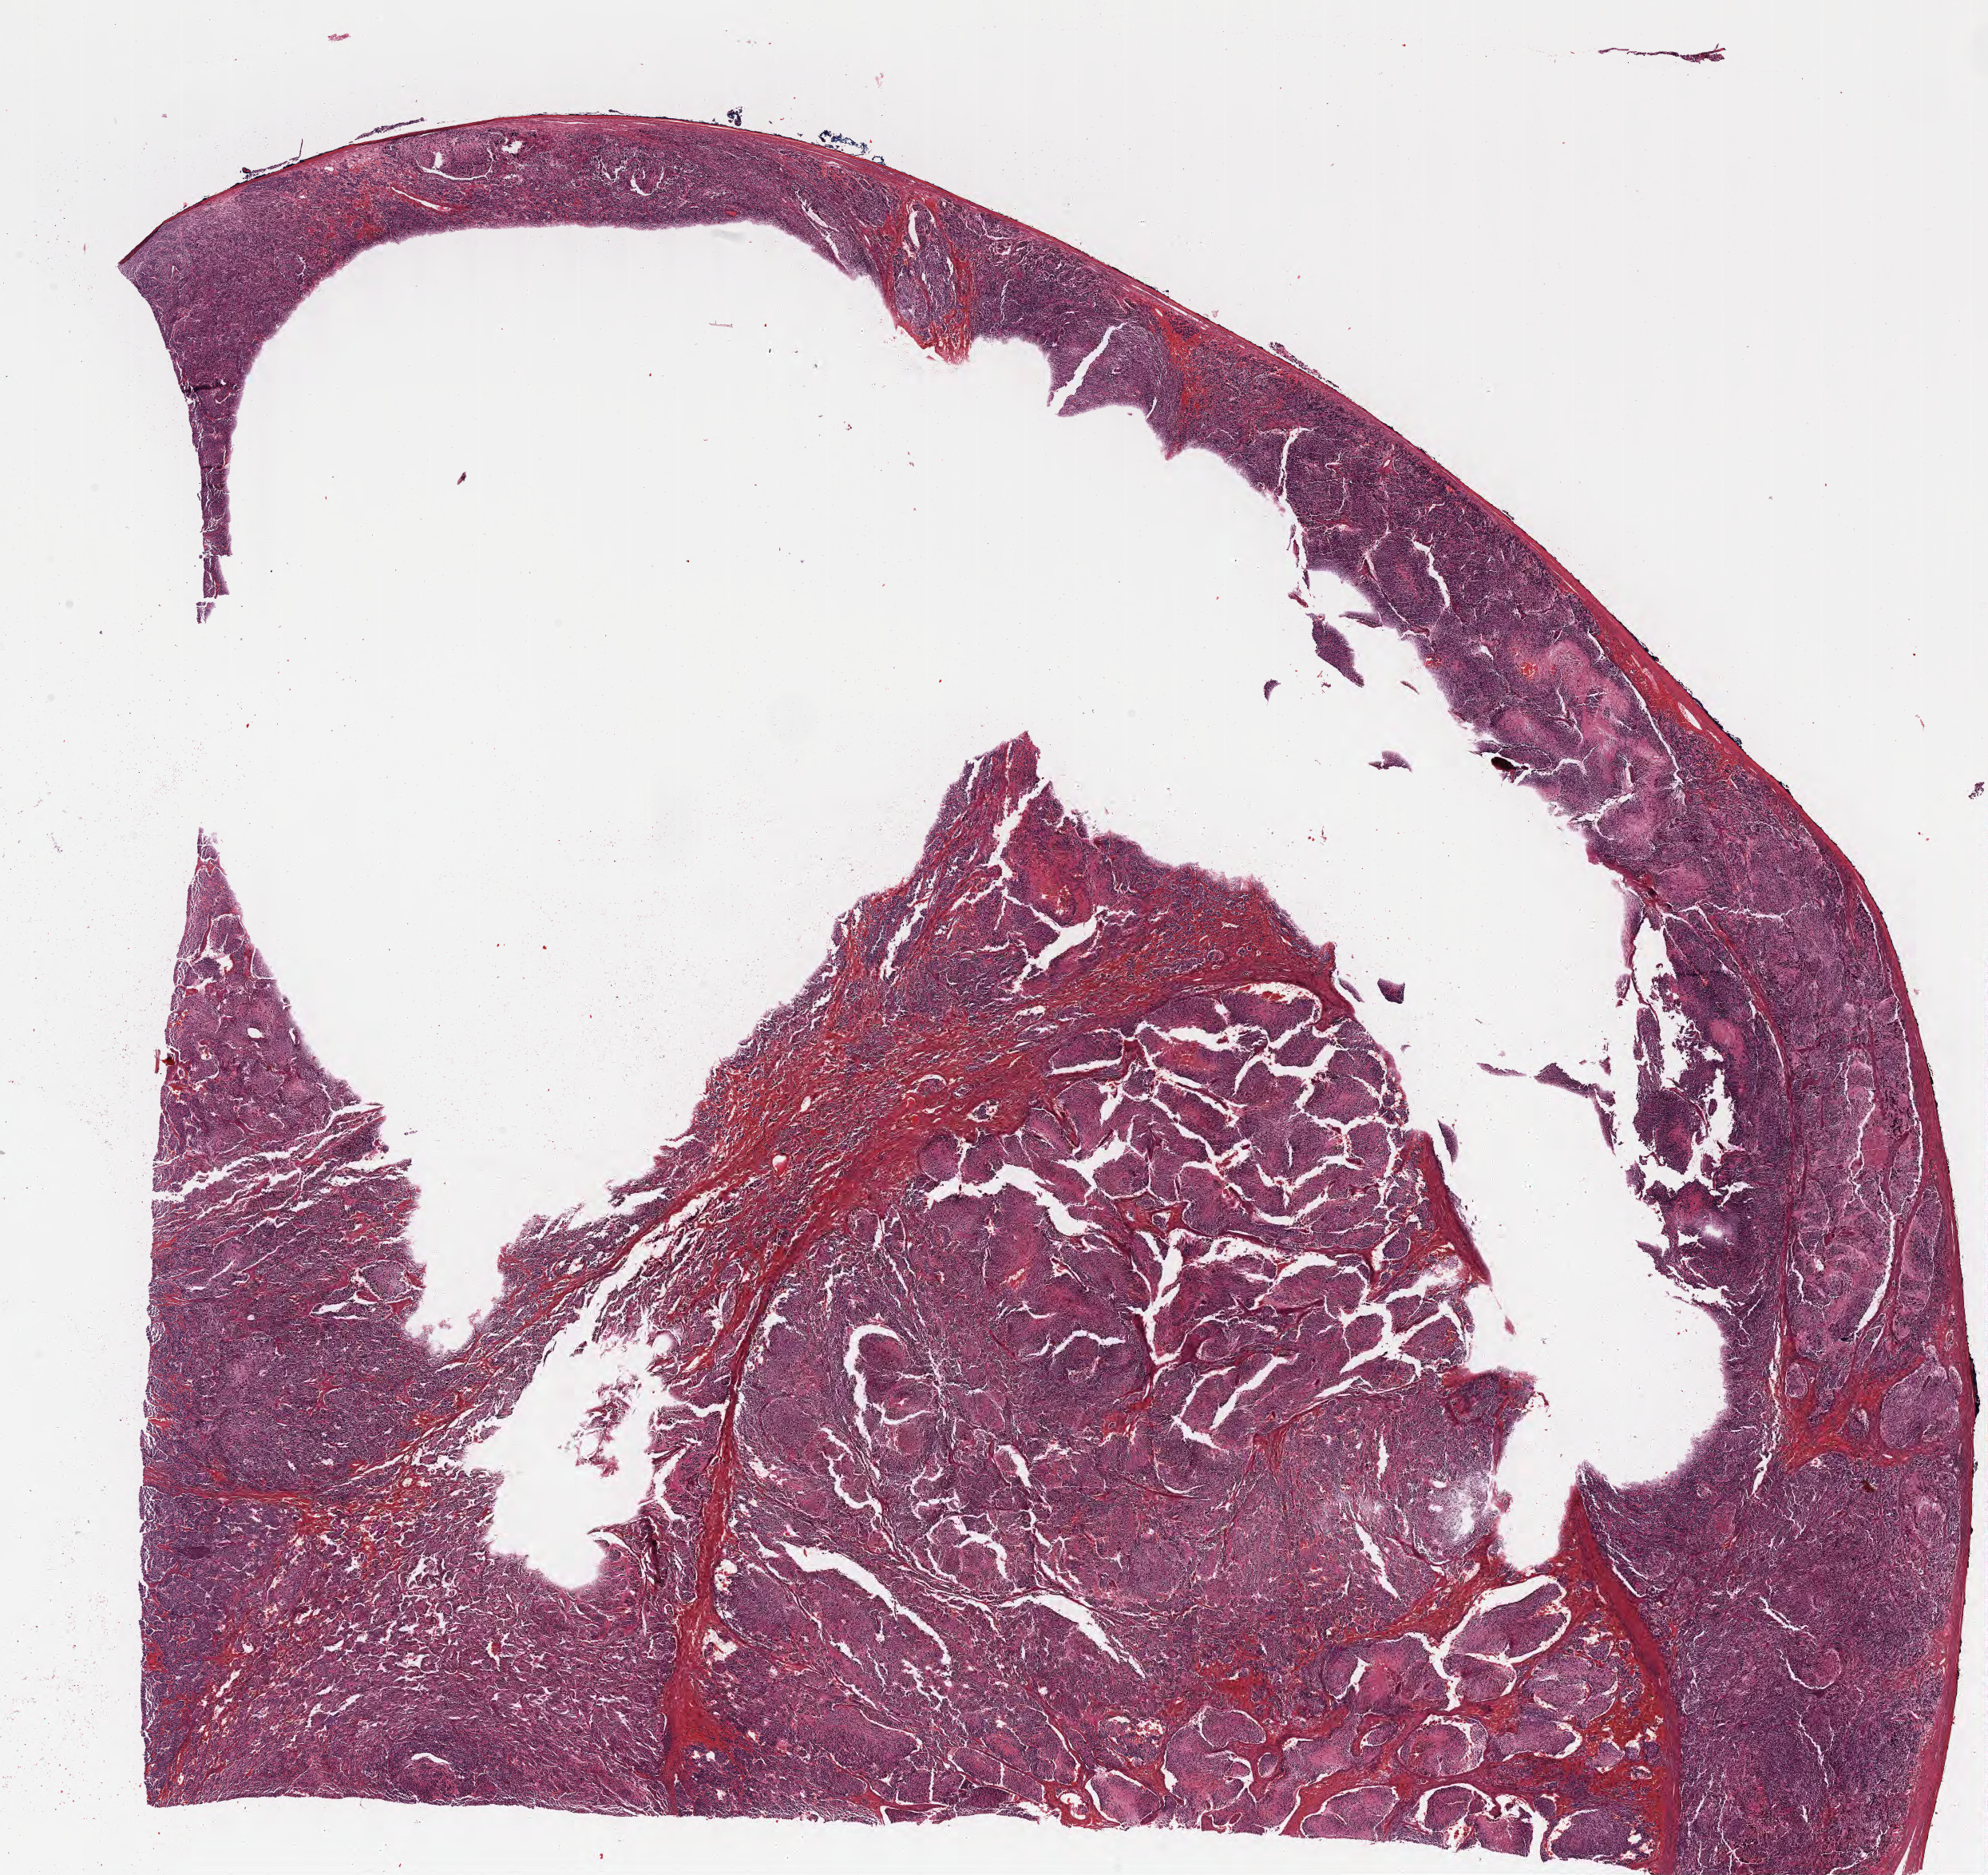
Whole-slide image, hematoxylin and eosin (H&E) stain of tumor tissue from the adrenal gland, shown as a low-resolution overview of the whole scanned area (about 20.1 x 19.0 mm), formalin-fixed, paraffin-embedded (FFPE) tissue. Male patient, age 428 days (about 1.2 years).
Diagnosis: Neuroblastoma, NOS.